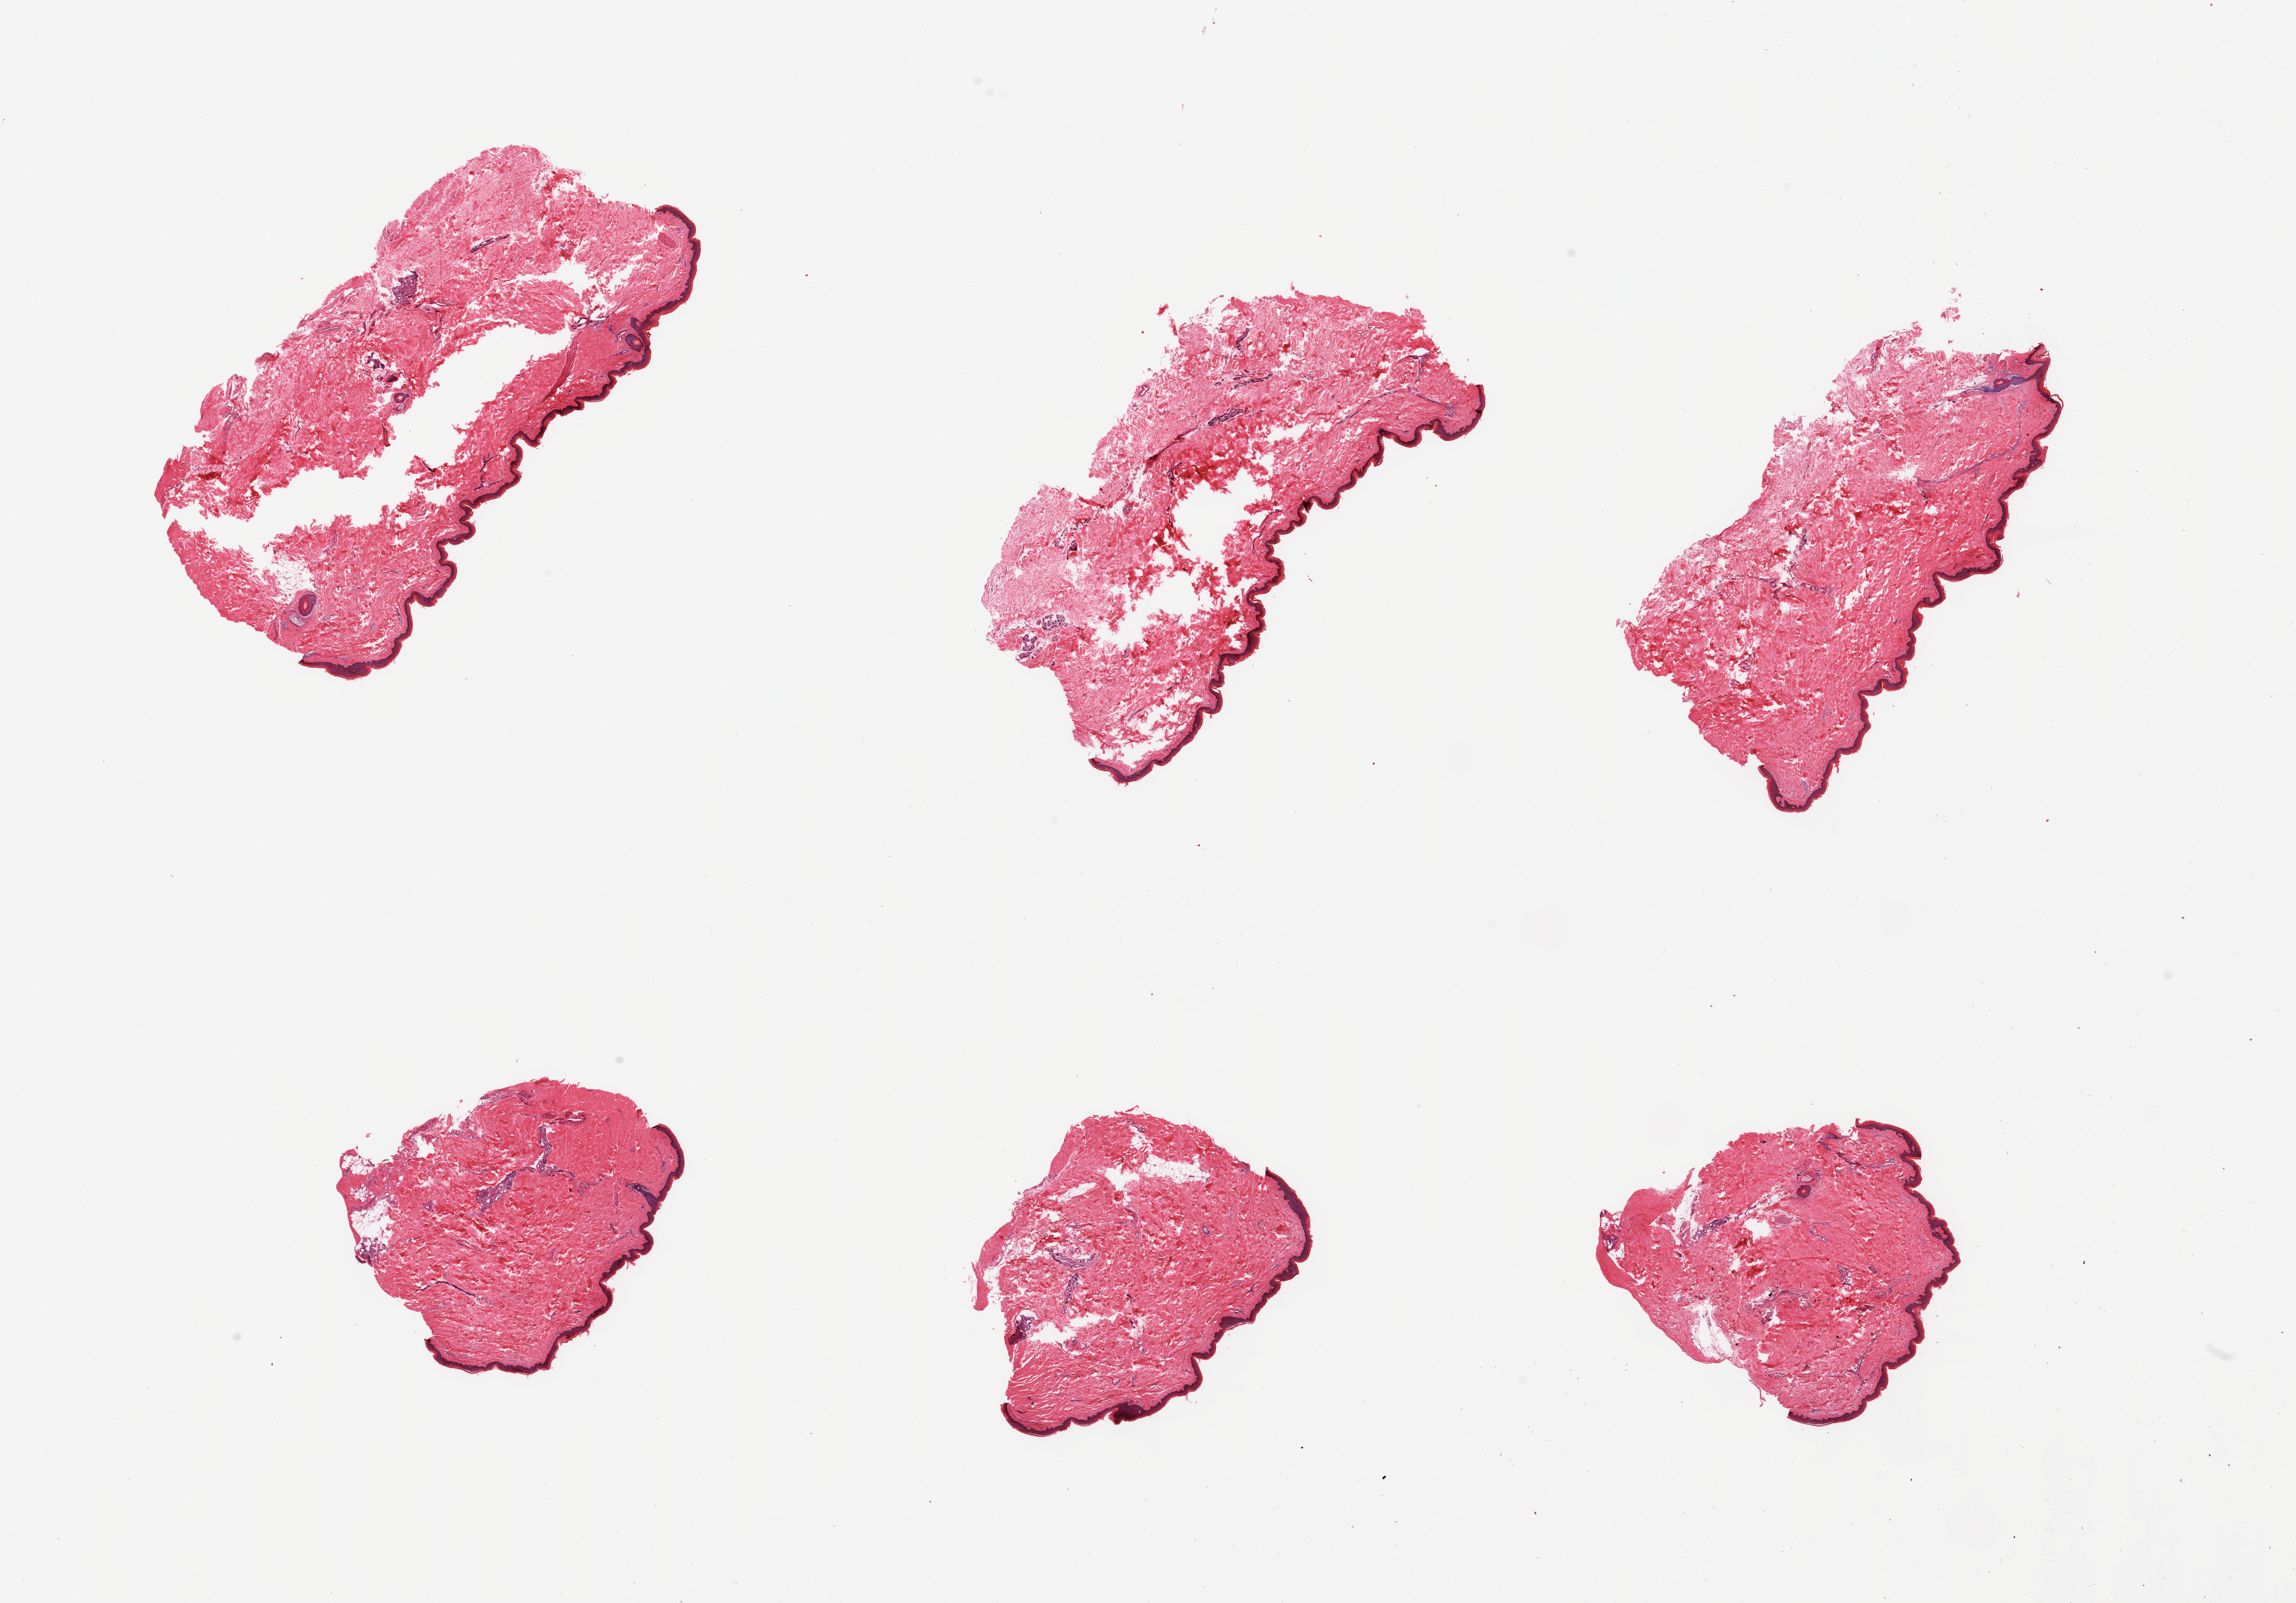
Whole-slide image, H&E stain, low-resolution overview of the scanned area, about 26.6 x 18.6 mm, PAXgene-fixed, paraffin-embedded tissue, section of skin of lower leg (target tissue), tissue donor sample. Donor sex: female.
Pathologist's review note for this sample: 6 pieces; well trimmed, only trivial fat, epidermis measures 44 microns.